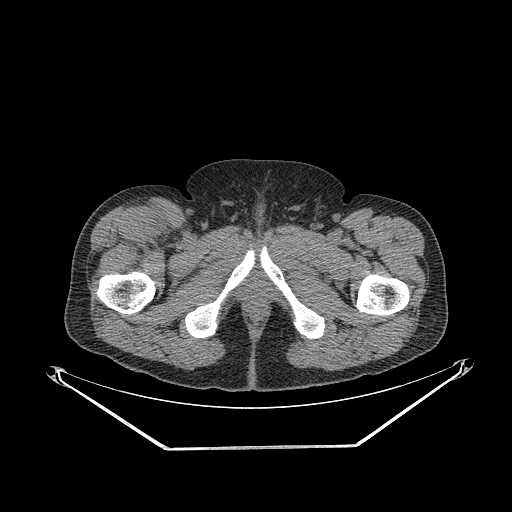
CT of an extremity soft-tissue mass (from a PET/CT study), one axial slice. Slice 307 of 311 in the series (ordered by position). 140 kVp. Soft-tissue window (W 400 / L 40 HU). 512 × 512 image matrix. Male patient. From the clinical record (not read from this slice): histological type: pleiomorphic leiomyosarcoma; grade: intermediate; site of the primary tumour: right thigh.
Annotated regions visible in this slice (expert contour drawn on MRI and transferred to this co-registered scan by the dataset authors):
- gross tumour volume including surrounding oedema: box from (x=141, y=208) to (x=170, y=239) px